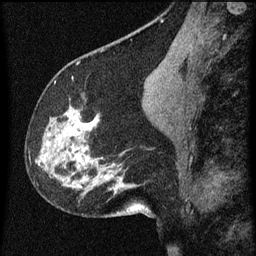
Breast MRI (dynamic contrast-enhanced), one sagittal slice. Slice 29 of 60 in the series (ordered by position). Dynamic contrast-enhanced series, image 2 of 3 at this slice position (ordered by acquisition). 1.5 T. TE 4.2 ms, TR 8 ms. 2 mm slice thickness. 256 × 256 image matrix, field of view 180 × 180 mm. Female patient, age 61 years.
Annotated regions visible in this slice (semi-automatically segmented with operator editing):
- analysis volume of interest (the breast-tissue region the enhancement analysis was run in; not a lesion): bounding box [x1, y1, x2, y2] px = [29, 80, 139, 209]
- tumour enhancement mask (voxels above the 70 % enhancement threshold inside the analysis volume of interest): [74, 122, 87, 161]